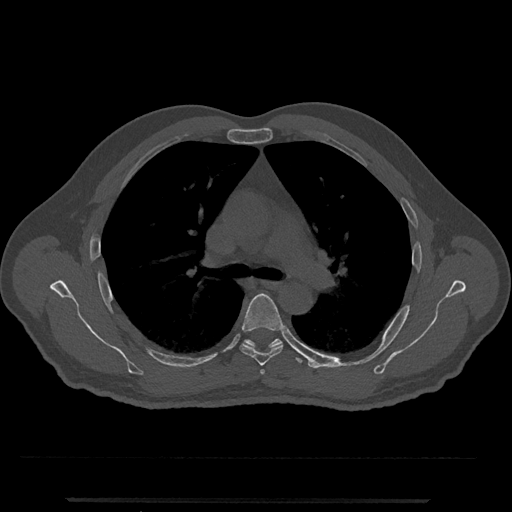
CT including the spine, one axial slice. Position 778 of 797 along the scan axis. Reconstruction kernel Br40s/3. 120 kVp. Bone window (W 1800 / L 400 HU). 0.5 mm slice thickness. 512 × 512 image matrix, field of view 419 × 419 mm. Male patient, age 63 years. Case-level facts recorded for this patient, not image findings: primary cancer: prostate.
Structures marked on this image (semi-automatically segmented with operator editing):
- T5 vertebra: bounding box <239,293,284,366> (left, top, right, bottom; pixels)
- T6 vertebra: <244,338,303,364>